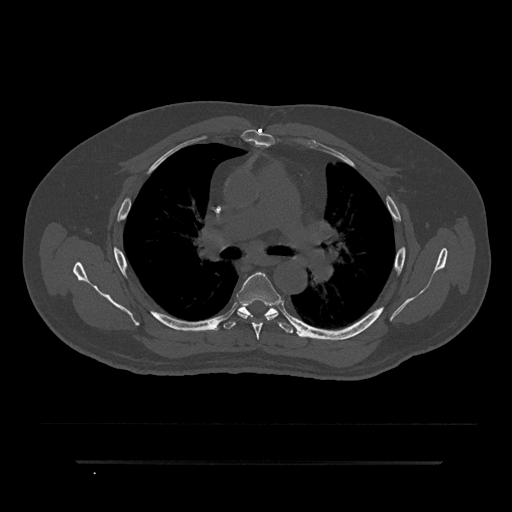
CT including the spine, one axial slice; slice 557 of 797 in the series (ordered by position); reconstruction kernel Br40s/3; 120 kVp; bone window (W 1800 / L 400 HU); 512 × 512 image matrix, field of view 464 × 464 mm. Male patient, age 59 years. Case-level facts recorded for this patient, not image findings: primary cancer: bile ducts.
Annotated regions visible in this slice (semi-automatic segmentation, software-assisted and operator-edited):
- T5 vertebra: bounding box [x1, y1, x2, y2] px = [237, 272, 279, 340]
- T6 vertebra: [223, 299, 293, 333]